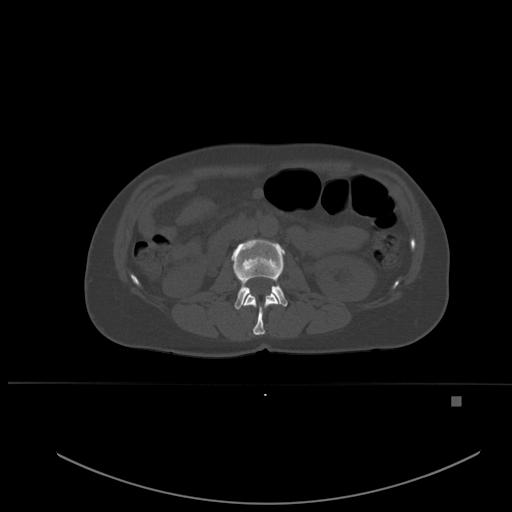
CT including the spine, one axial slice; bone window (W 1800 / L 400 HU); 1.5 mm slice thickness; 512 × 512 image matrix, field of view 443 × 443 mm. Patient: female, 49 years. From the clinical record (not read from this slice): primary cancer: breast; vertebrae with lytic lesions (as recorded): L3, T12, L4.
Structures marked on this image (semi-automatically segmented with operator editing):
- L1 vertebra: bounding box <243,292,279,335> (left, top, right, bottom; pixels)
- L2 vertebra: <231,239,288,310>